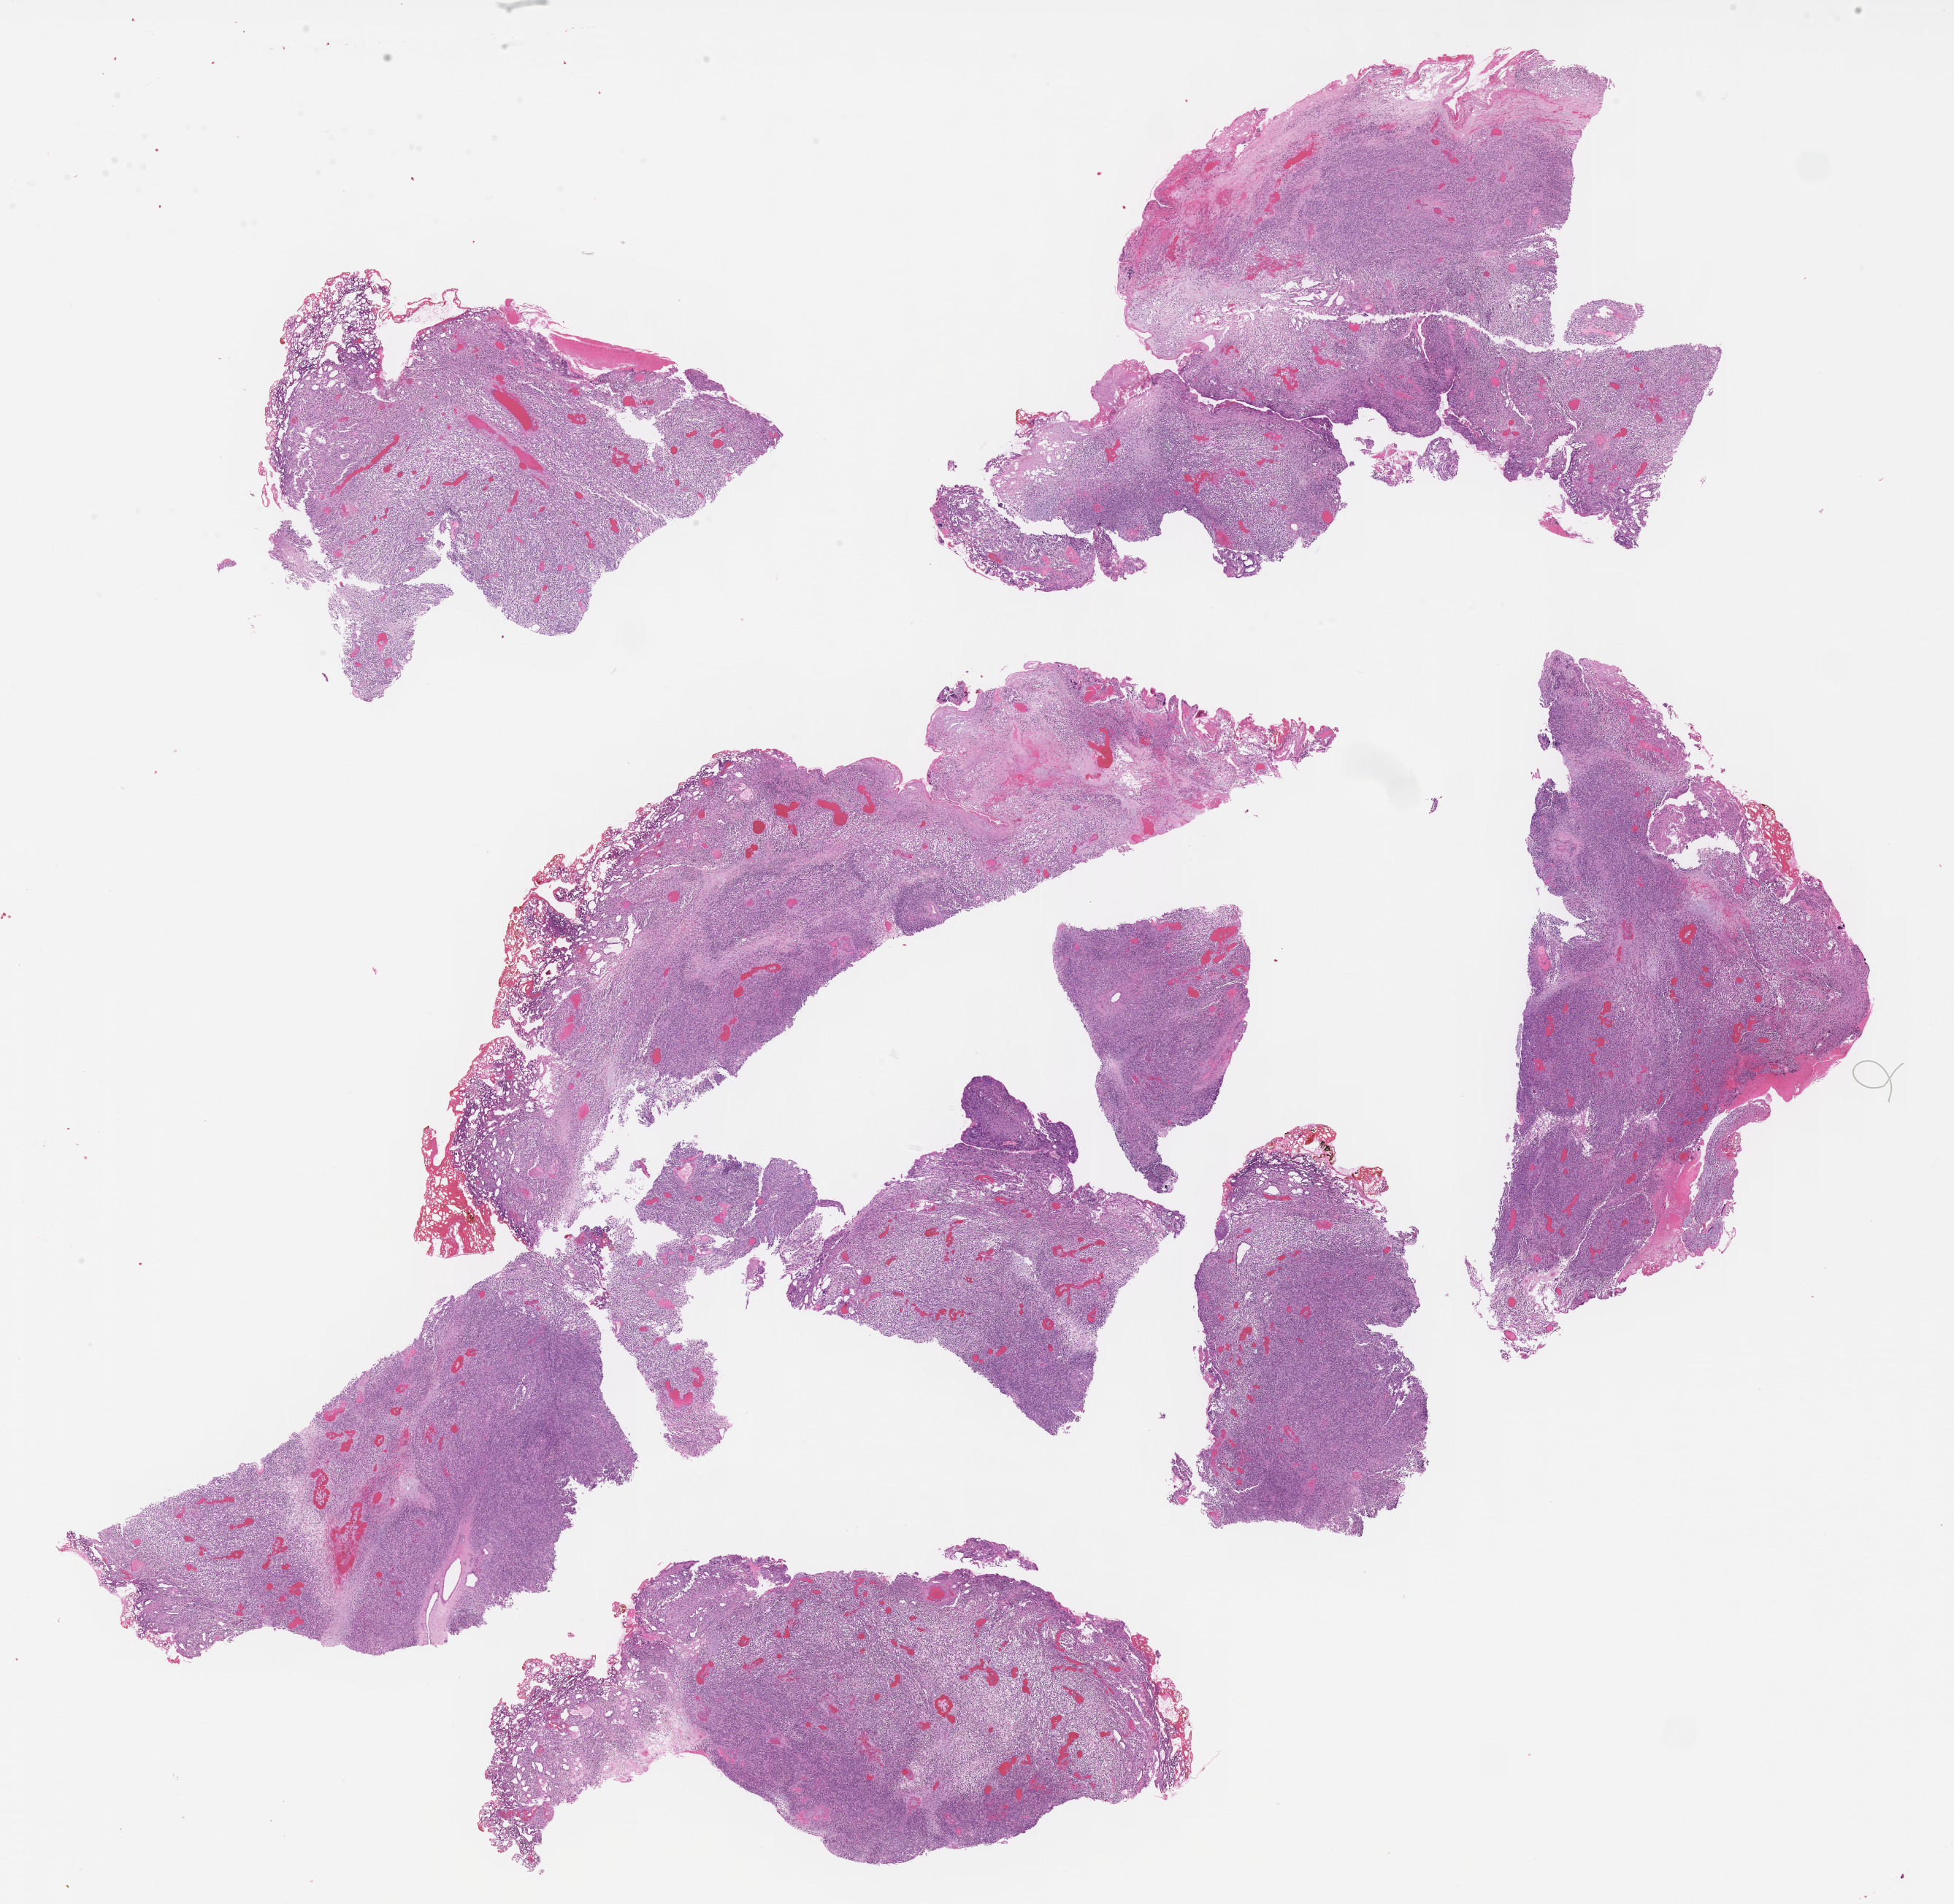
Whole-slide image, hematoxylin and eosin (H&E) stain of tumor tissue, whole scanned area (about 21.6 x 21.1 mm) shown as a low-resolution overview. FFPE section. Site: soft tissue, pelvis. Male patient, age at diagnosis 3.8 years.
Metastatic status at presentation (as recorded): non-metastatic (confirmed). Stage (as recorded): 3. Diagnosis: rhabdomyosarcoma; histological classification: embryonal rhabdomyosarcoma.